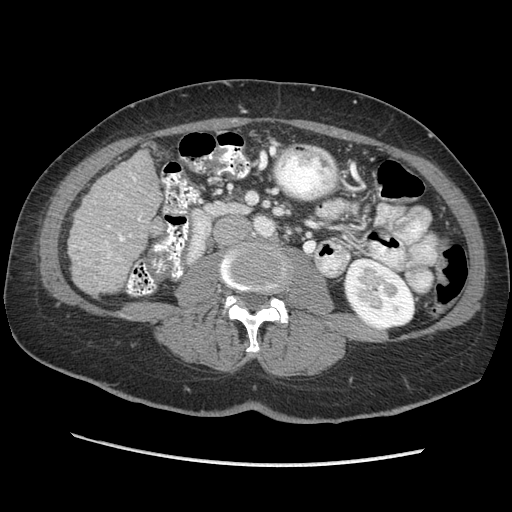
Contrast-enhanced abdominal CT (liver protocol), one axial slice. Slice 95 of 170 in the series (ordered by position). Reconstruction kernel STANDARD. 140 kVp. Soft-tissue window (W 400 / L 40 HU). 2.5 mm slice thickness. 512 × 512 image matrix, field of view 360 × 360 mm. From the clinical record (not read from this slice): diagnosis: hepatocellular carcinoma (patient treated with transarterial chemoembolisation; whether this scan precedes or follows treatment is not stated here); TNM stage (as recorded): Stage-II; Child-Pugh class: A.
Structures marked on this image (semi-automatic segmentation, software-assisted and operator-edited):
- liver parenchyma outside the tumour (the mass and vessels are separate outlines, so this box may not span the whole liver): bounding box (x1, y1, x2, y2) in pixels: (68, 150, 160, 294)
- liver vessels: (80, 177, 140, 258)